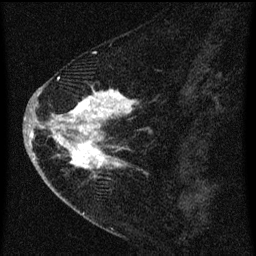
Breast MRI (dynamic contrast-enhanced), one sagittal slice; slice 24 of 60 in the series (ordered by position); dynamic contrast-enhanced series, image 2 of 3 at this slice position (ordered by acquisition); 1.5 T; TE 4.2 ms, TR 8 ms; 2 mm slice thickness; 256 × 256 image matrix, field of view 180 × 180 mm. Female patient, age 47 years.
Annotated regions visible in this slice (semi-automatic segmentation, software-assisted and operator-edited):
- analysis volume of interest (the breast-tissue region the enhancement analysis was run in; not a lesion): bounding box (x1, y1, x2, y2) in pixels: (38, 76, 156, 193)
- tumour enhancement mask (voxels above the 70 % enhancement threshold inside the analysis volume of interest): (39, 78, 136, 179)